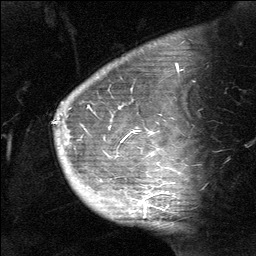
Breast MRI (dynamic contrast-enhanced), one sagittal slice. Slice 49 of 64 in the series (ordered by position). Dynamic contrast-enhanced study with each time point stored as its own series, time point 2 of 3 at this slice position (early post-contrast, ordered by acquisition time). 1.5 T. TE 4.8 ms, TR 27 ms. 256 × 256 image matrix, field of view 180 × 180 mm. Female patient, age 39 years. From the clinical record (not read from this slice): setting: breast cancer imaged before/during neoadjuvant chemotherapy; receptor status: HER2-positive.
Structures marked on this image (semi-automatic segmentation, software-assisted and operator-edited):
- analysis volume of interest (the breast-tissue region the enhancement analysis was run in; not a lesion): bounding box (x1, y1, x2, y2) in pixels: (58, 40, 199, 217)
- tumour enhancement mask (voxels above the 90 % enhancement threshold inside the analysis volume of interest): (122, 70, 179, 207)